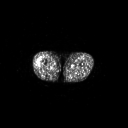
FDG PET of an extremity soft-tissue mass (from a PET/CT study), one axial slice. Position 222 of 267 along the scan axis. 3.27 mm slice thickness. 128 × 128 image matrix, field of view 700 × 700 mm. Patient: male, 43 years. Case-level facts recorded for this patient, not image findings: histological type: poorly differentiated synovial sarcoma; grade: high; site of the primary tumour: right buttock.
Structures marked on this image (expert contour drawn on MRI and transferred to this co-registered scan by the dataset authors):
- gross tumour volume including surrounding oedema: bounding box (x1, y1, x2, y2) in pixels: (35, 60, 43, 67)